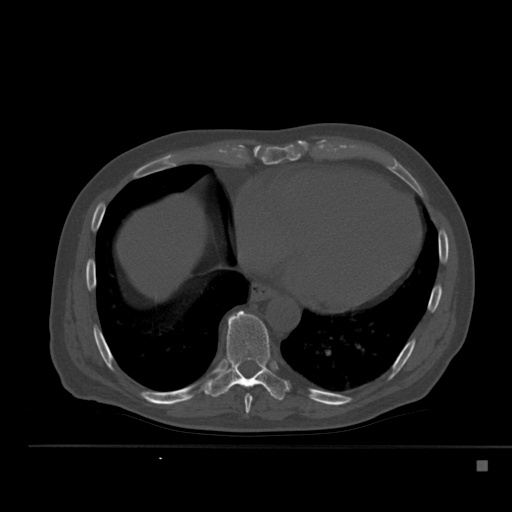
CT including the spine, one axial slice. 120 kVp. Bone window (W 1800 / L 400 HU). 1.5 mm slice thickness. 512 × 512 image matrix. Patient: male, 70 years. From the clinical record (not read from this slice): primary cancer: renal.
Outlined on this slice (semi-automatically segmented with operator editing):
- T8 vertebra: bounding box (x1, y1, x2, y2) in pixels: (244, 385, 255, 414)
- T9 vertebra: (207, 310, 290, 400)